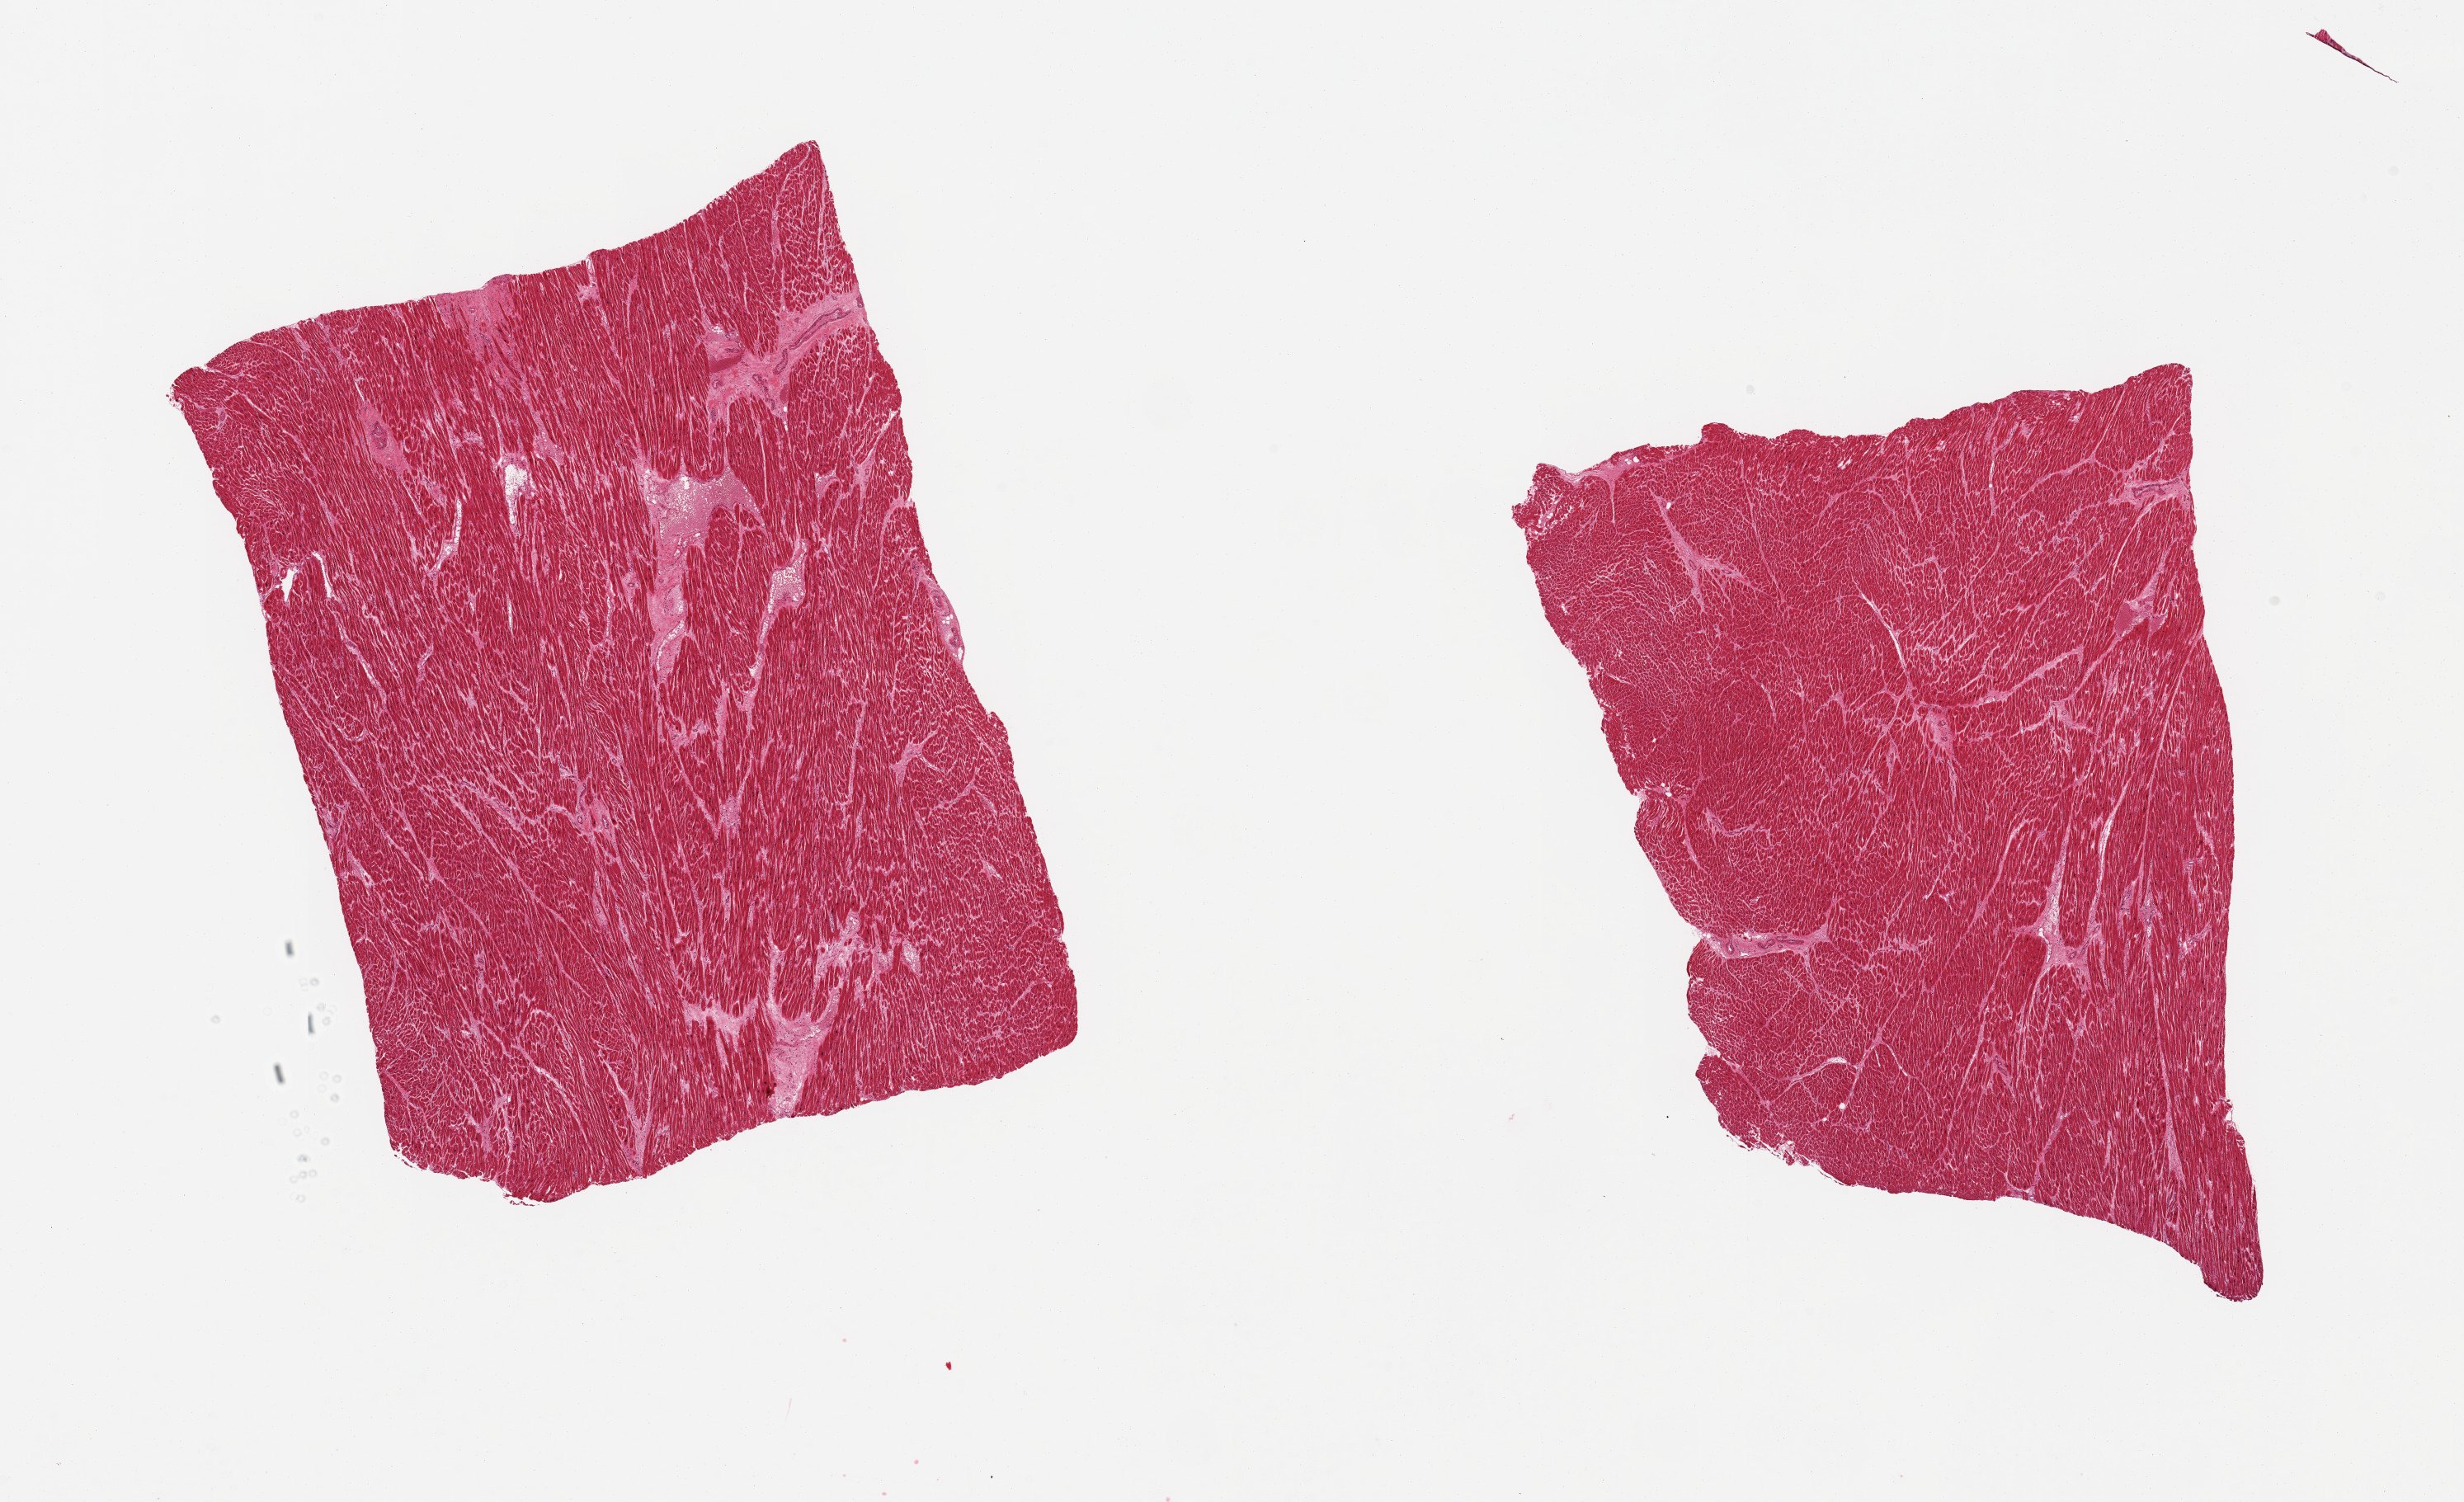
Whole-slide image, H&E stain, a low-resolution overview of the entire scanned area, about 23.6 x 14.4 mm, PAXgene-fixed paraffin-embedded (PFPE) section, sampled site (target tissue): heart, donor tissue sample.
Pathologist's review note for this sample: 2 piecesm moderate chronic ischemic changes/fibrosis, subacute cellular ischemic changes.